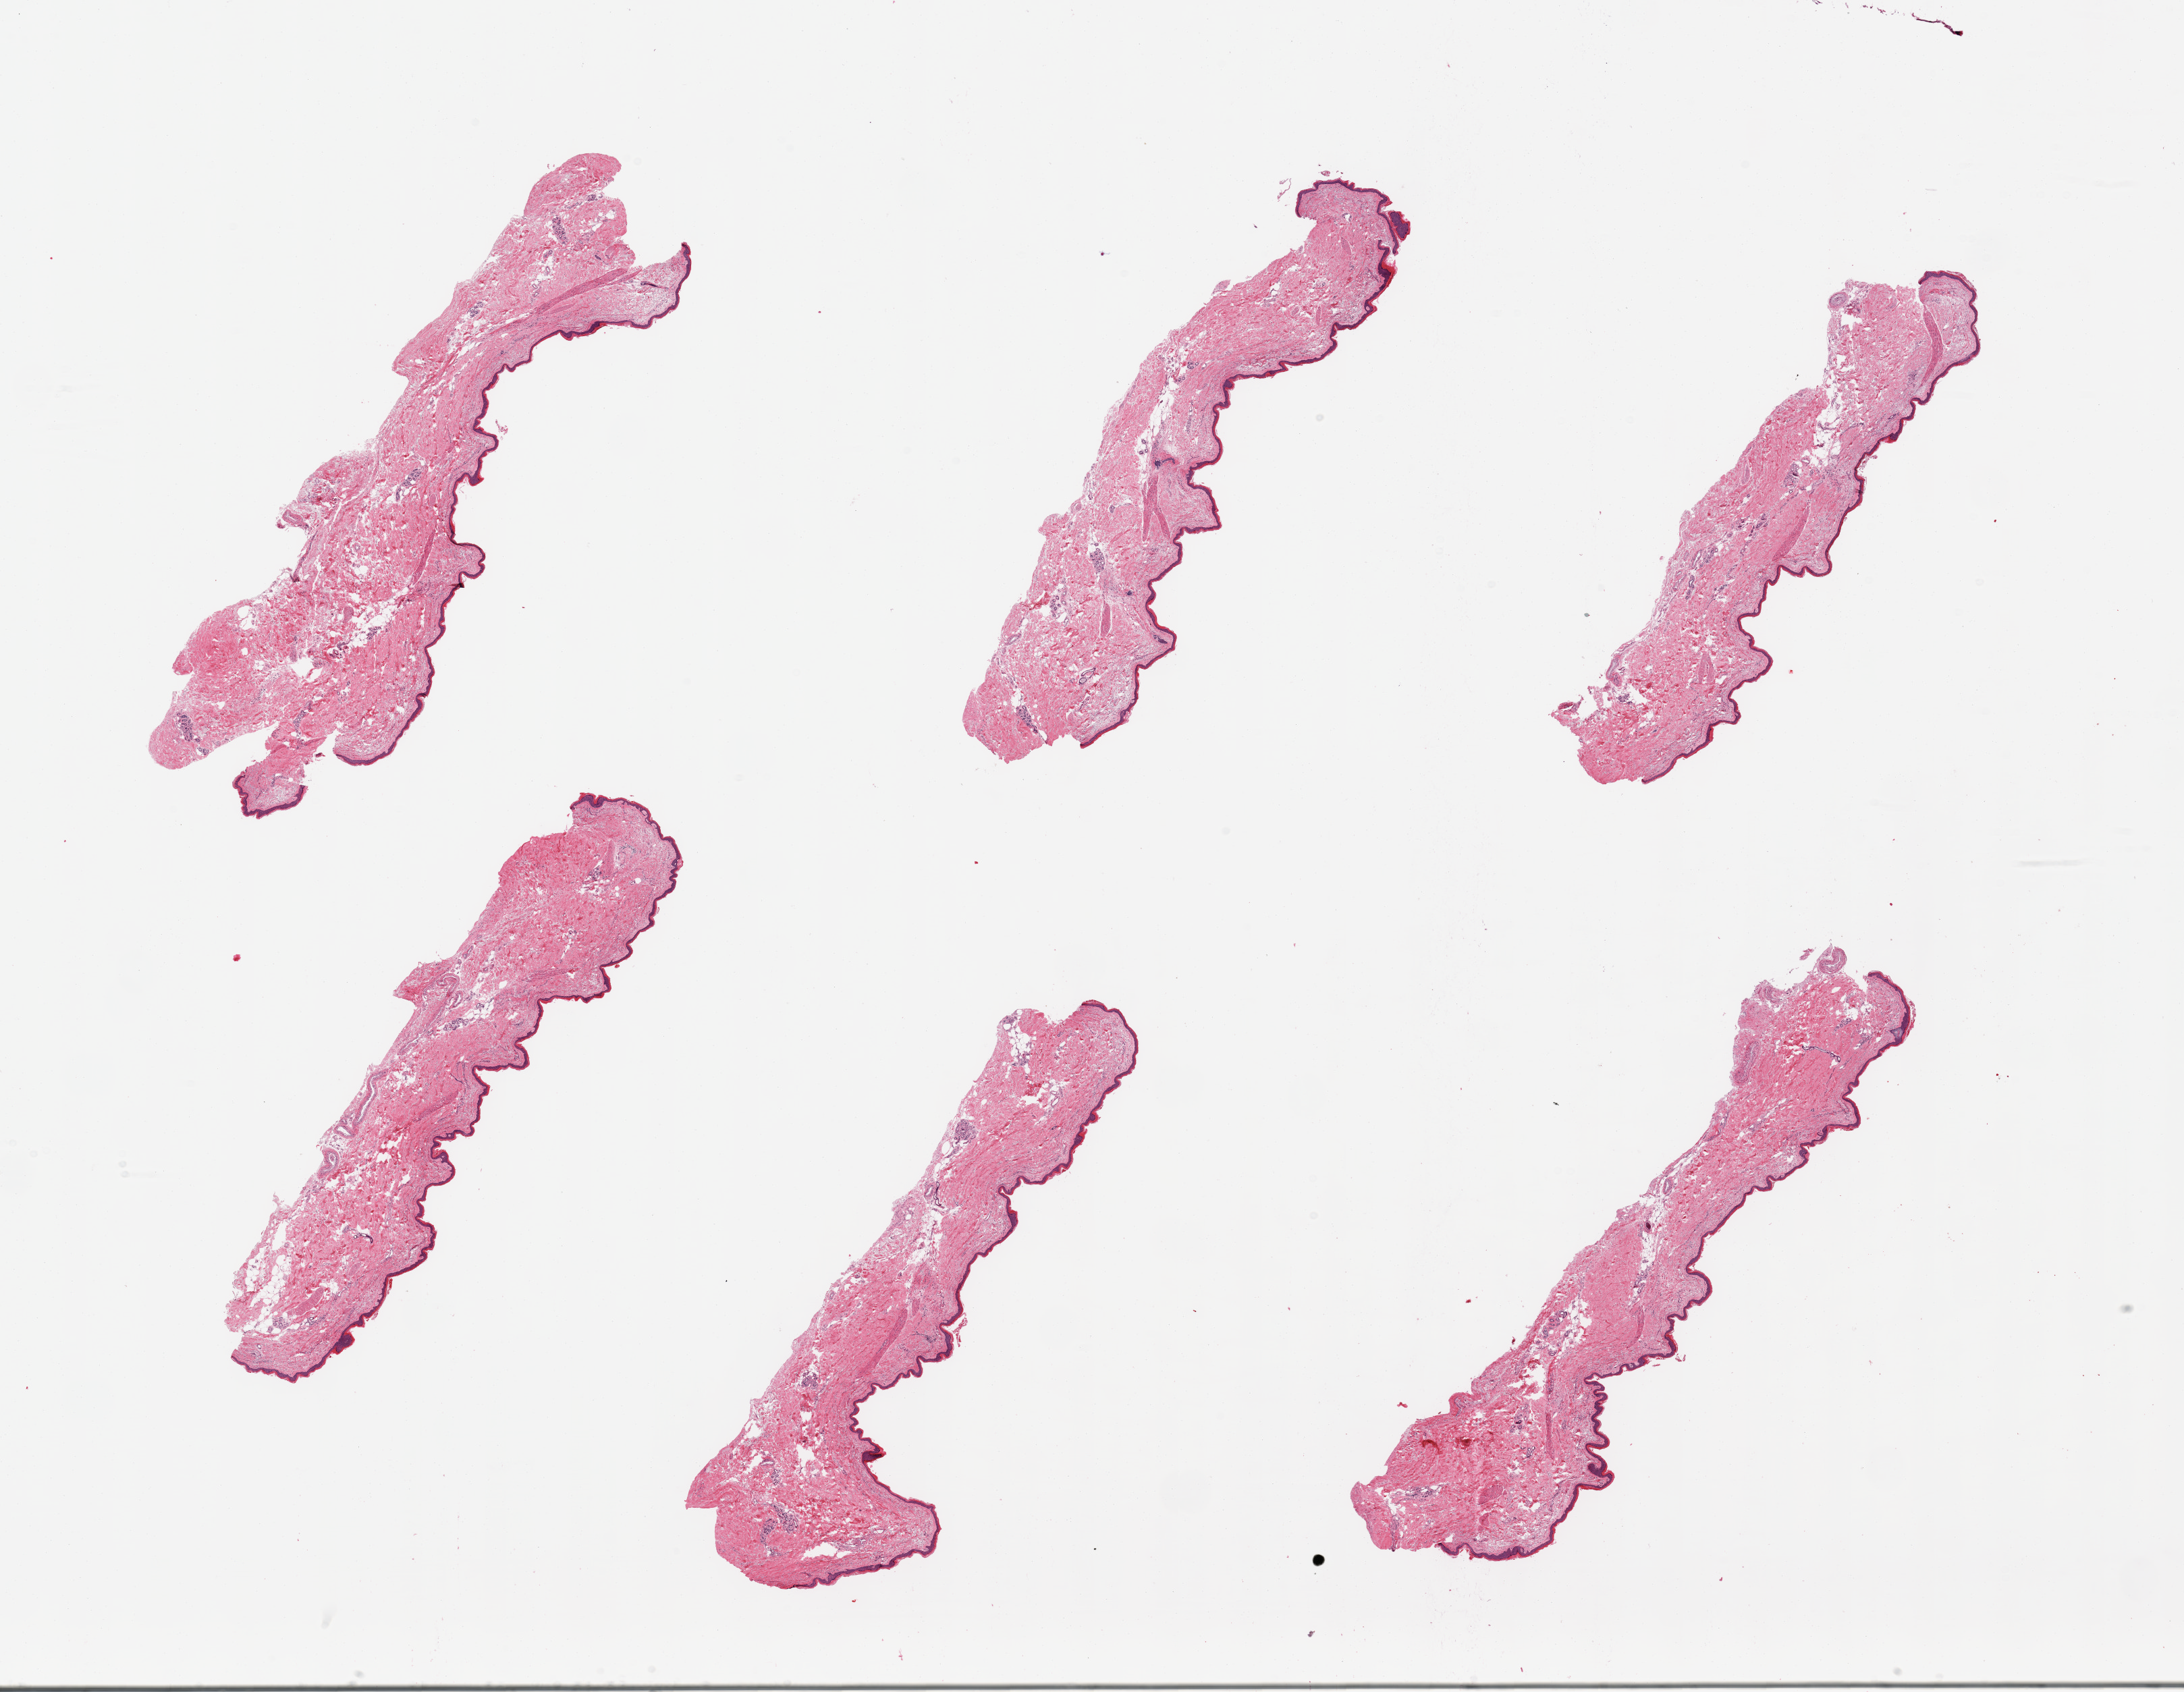
Whole-slide image, H&E stain, a low-resolution overview of the entire scanned area, about 25.6 x 19.8 mm (from a 20x scan). PAXgene-fixed paraffin-embedded (PFPE) section. Target tissue: skin of lower leg. Tissue donor sample. Male donor.
Review note (as recorded): 6 pieces; well trimmed; dermal fat up to 10%.